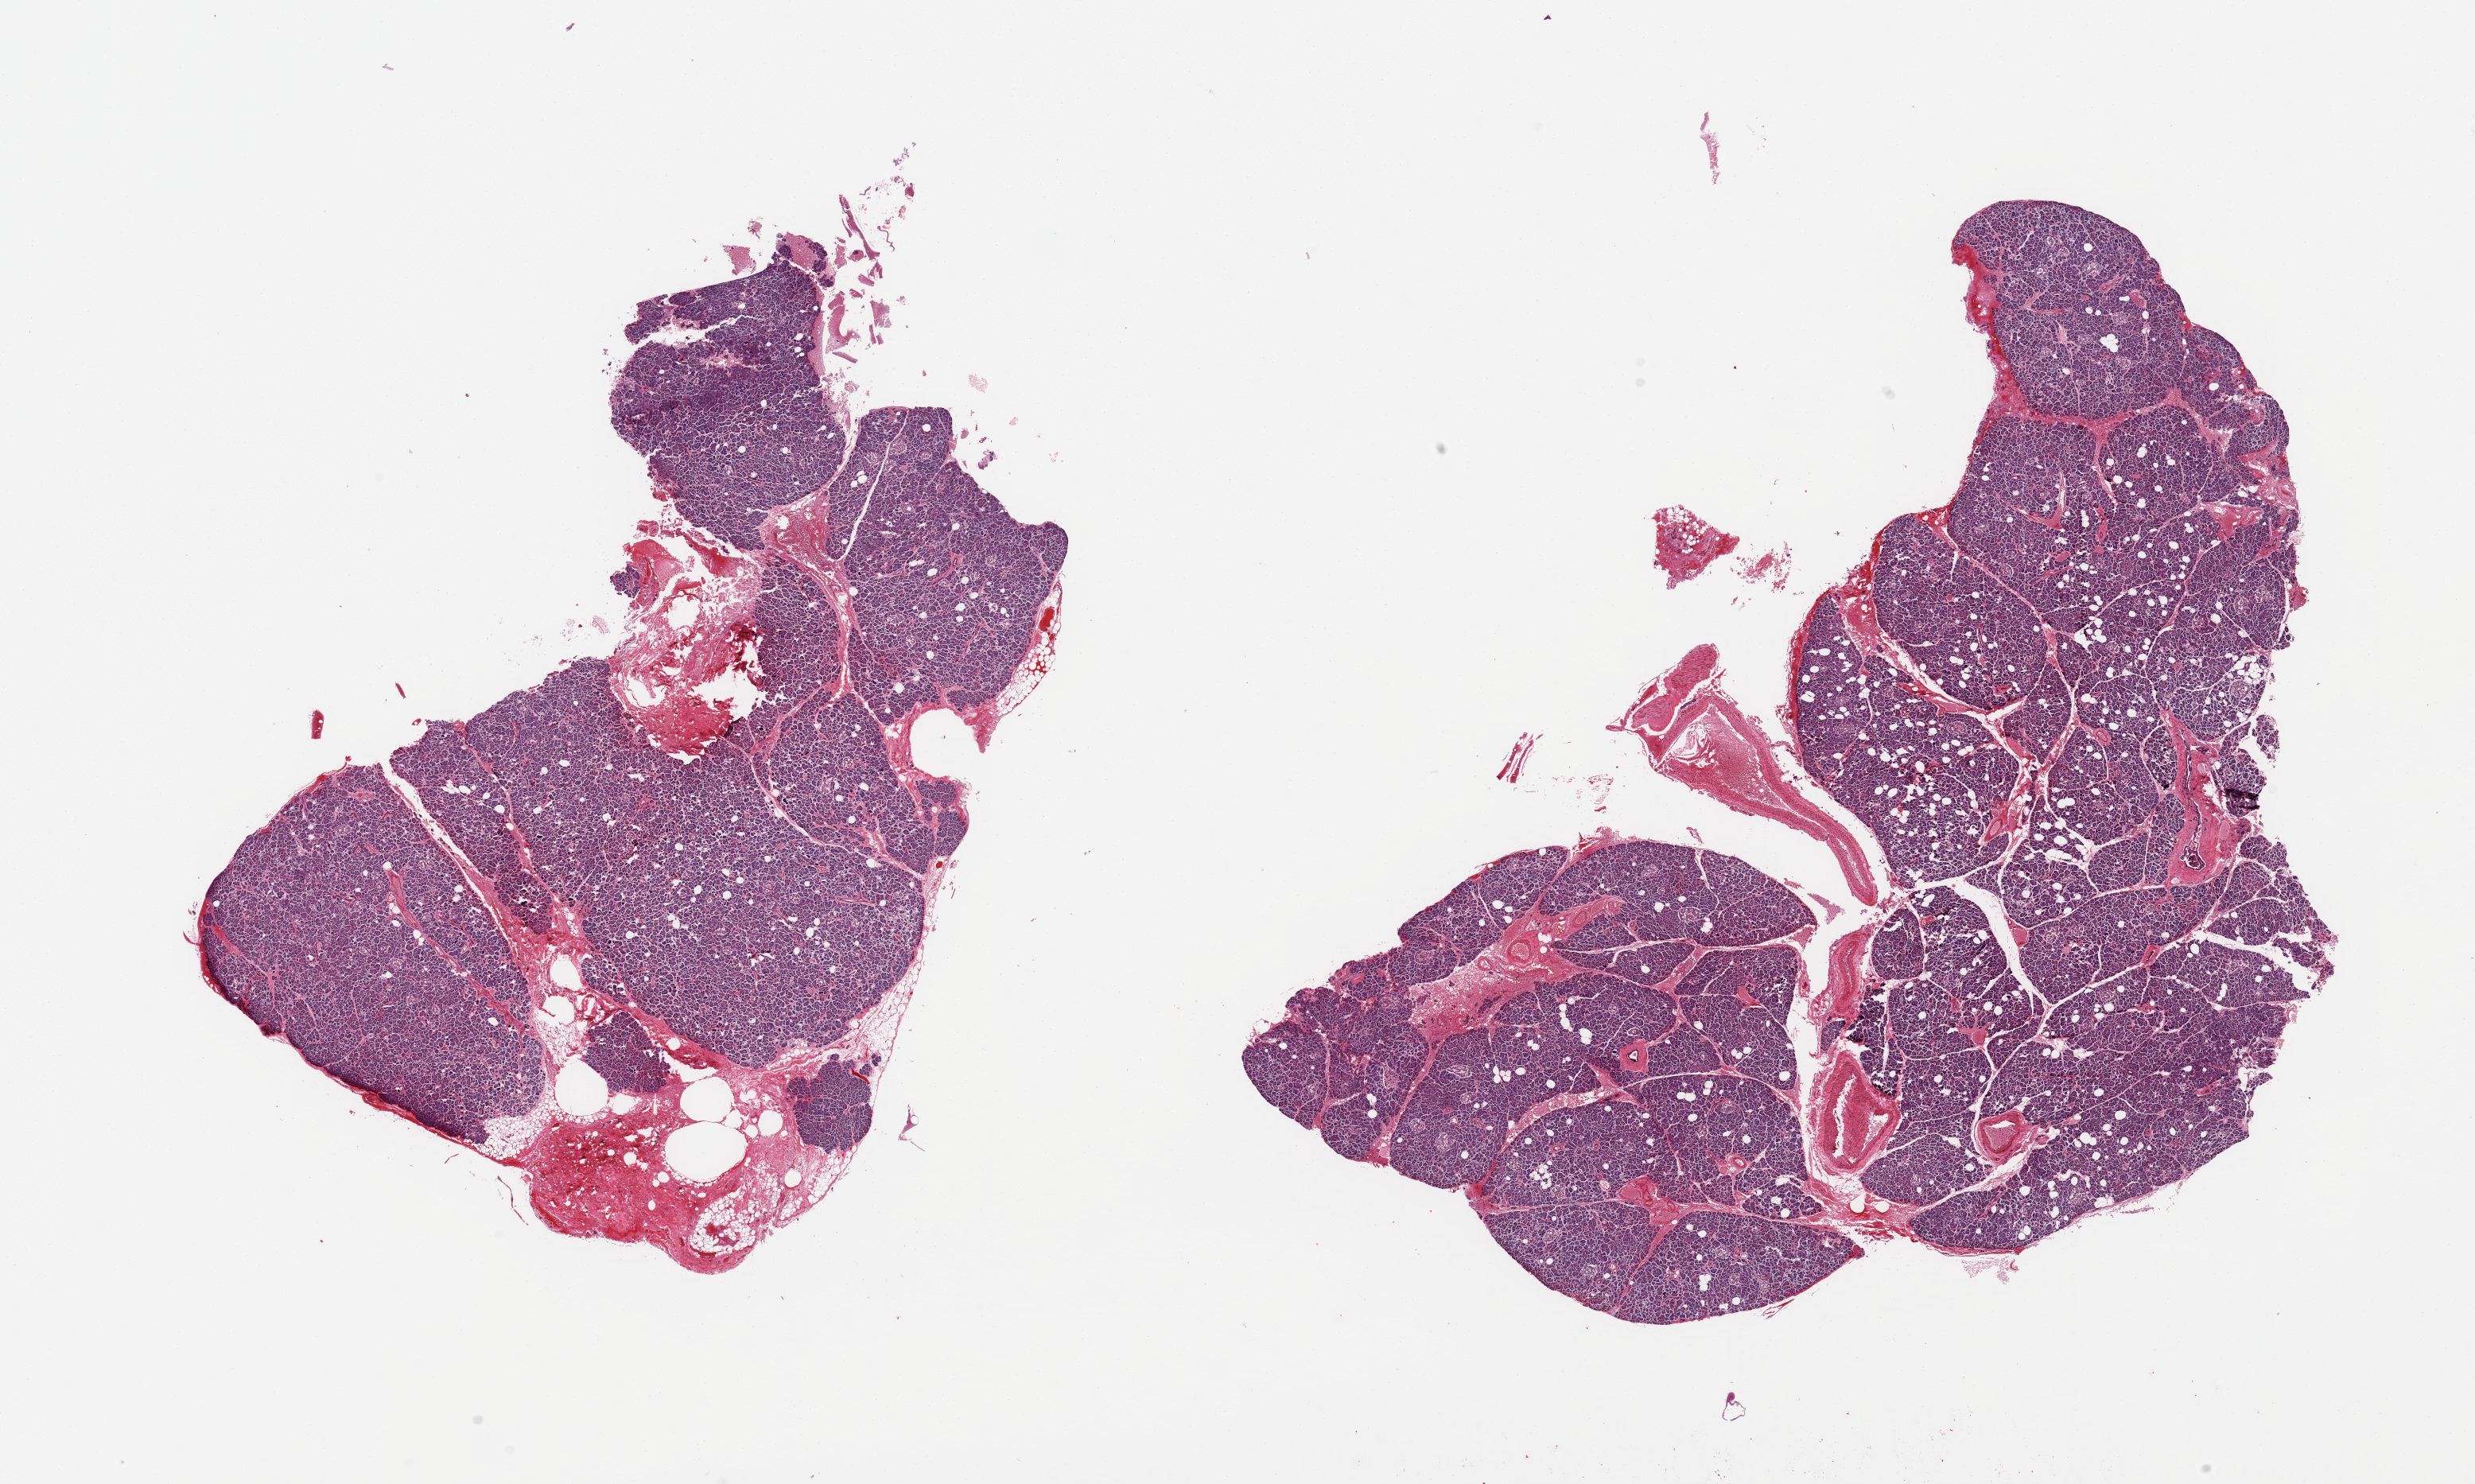
Whole-slide image, haematoxylin and eosin stain, brightfield — shown as a low-resolution overview of the whole scanned area (about 24.6 x 14.8 mm, from a 20x scan); PAXgene-fixed, paraffin-embedded tissue; sampled site (target tissue): adrenal gland; tissue donor sample. Donor sex: female.
Review note (as recorded): 2 pieces, pancreas, no adrenal present.